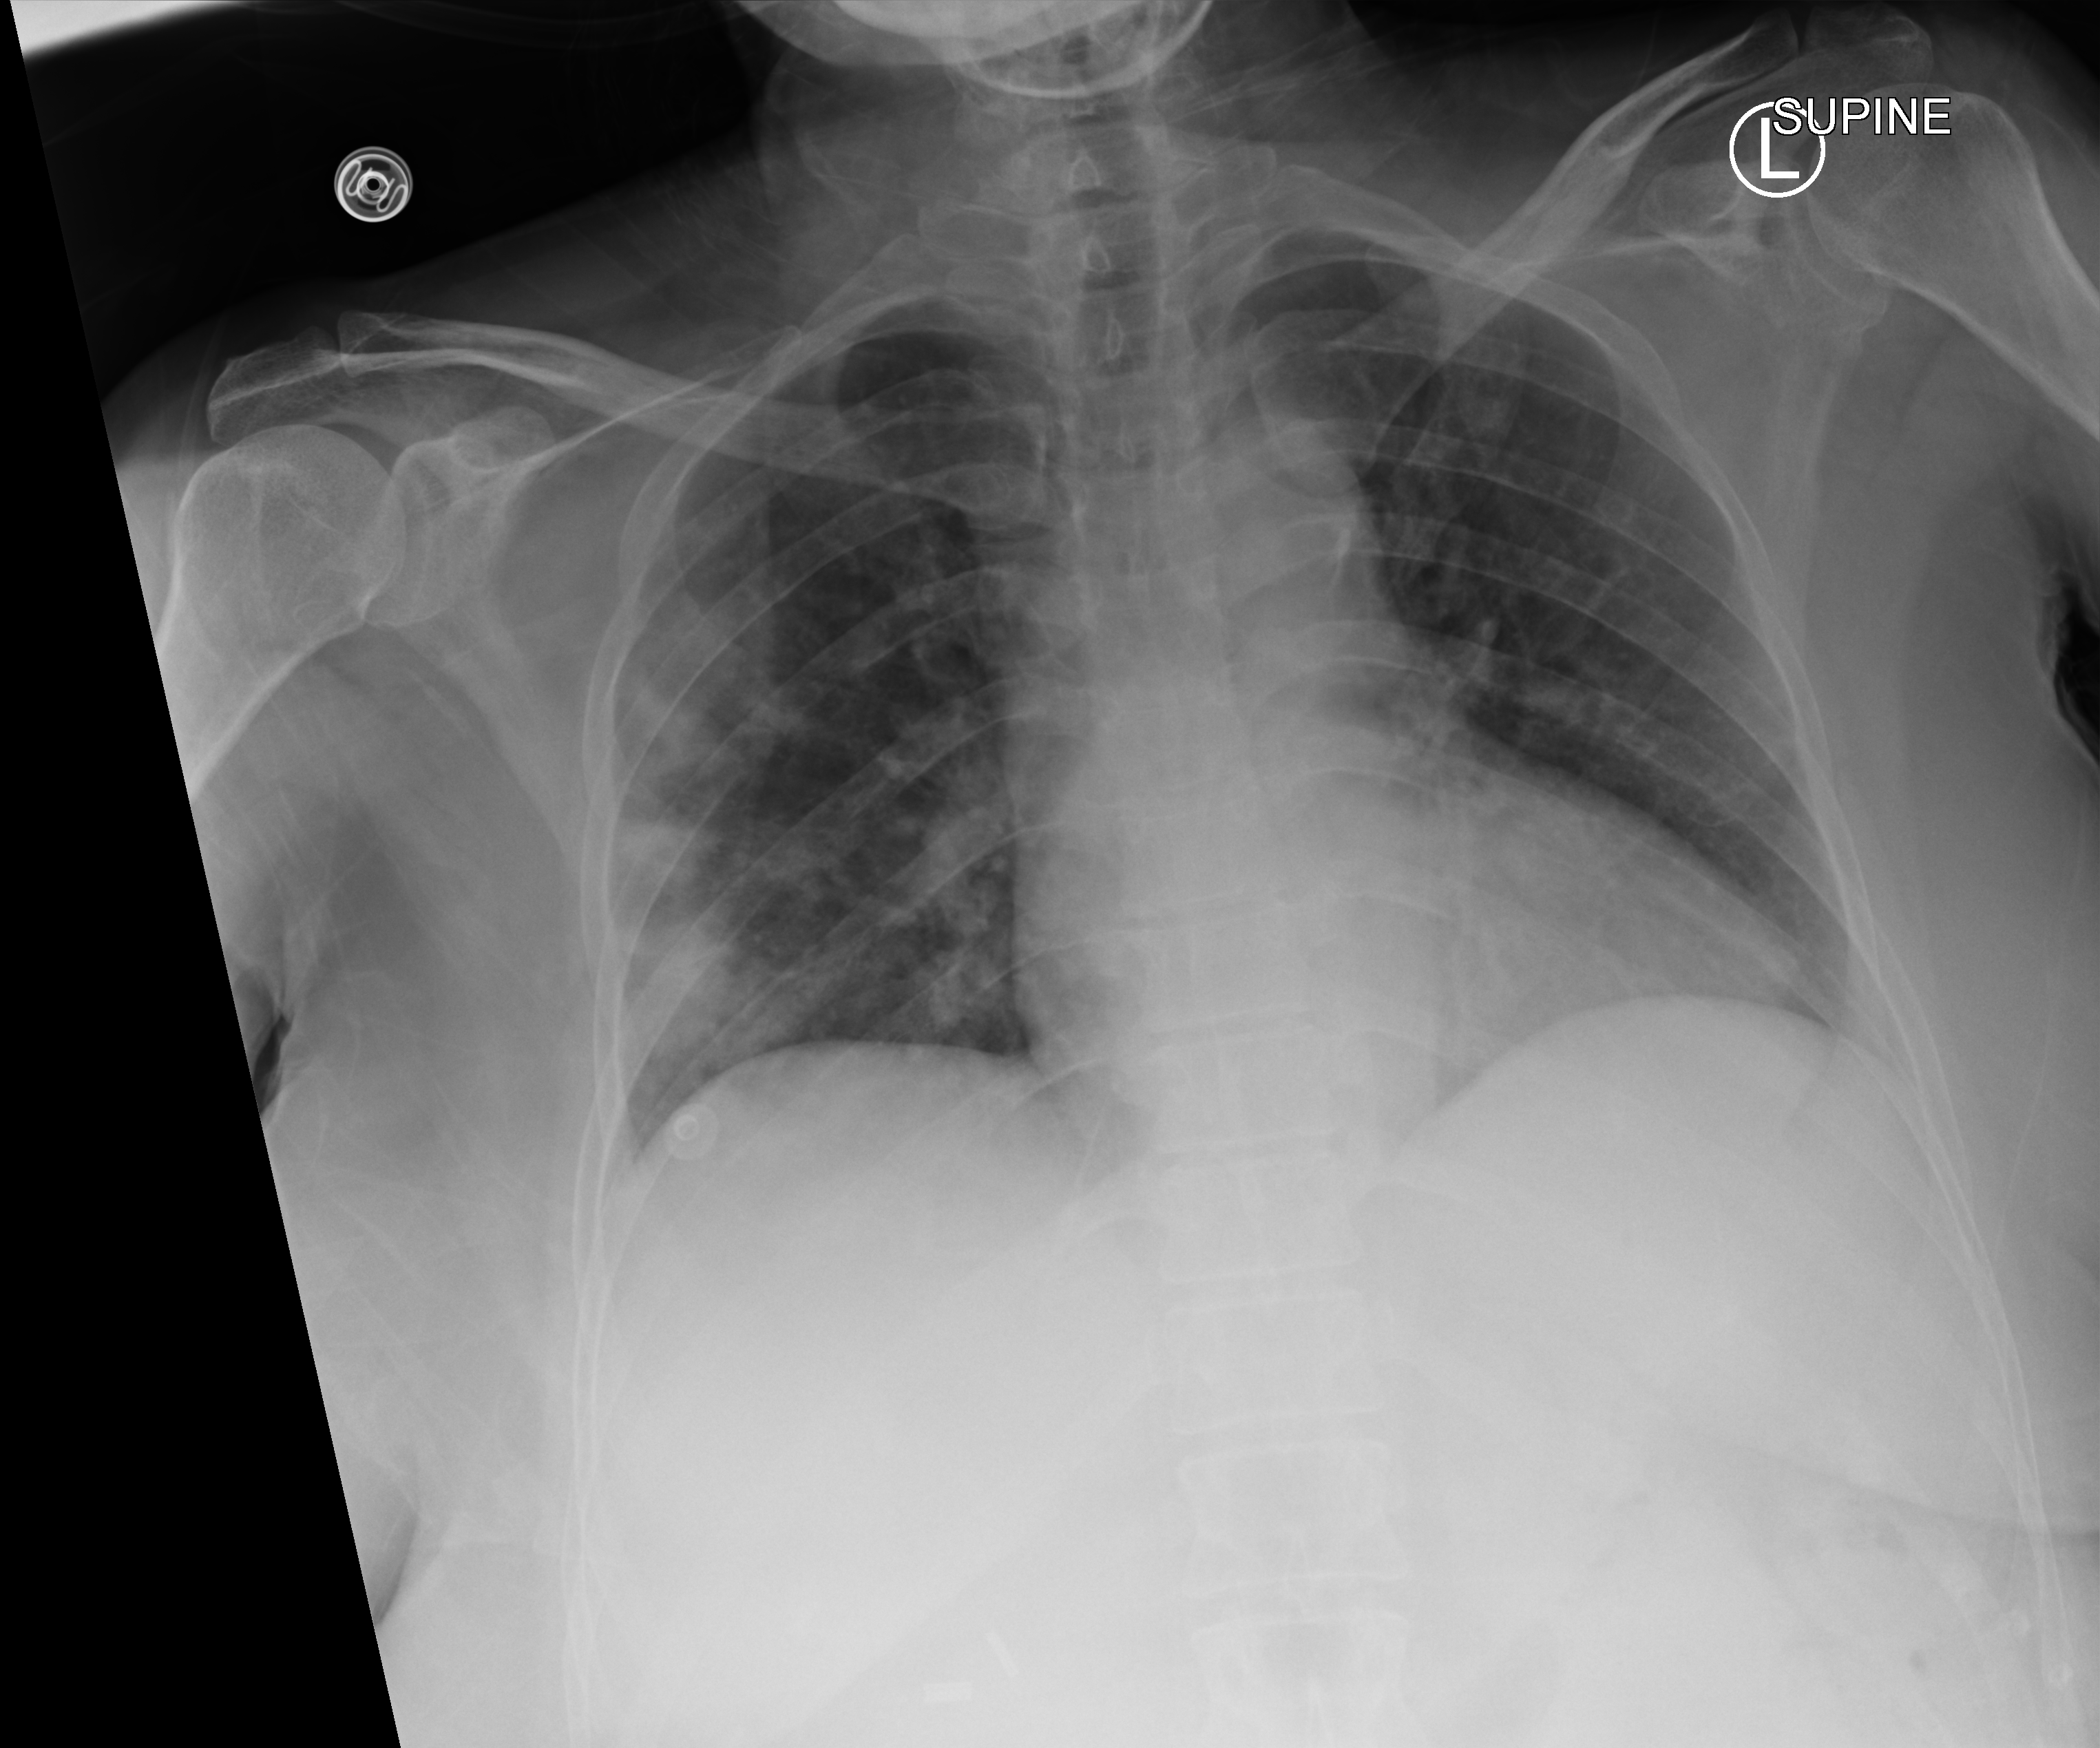
Chest X-ray (portable), anteroposterior (AP) projection. Female patient hospitalised with COVID-19, age 18–59 years.
Admission-level facts for this patient (not findings on this image; timing relative to this image not recorded): mechanically ventilated during this hospital stay: no.